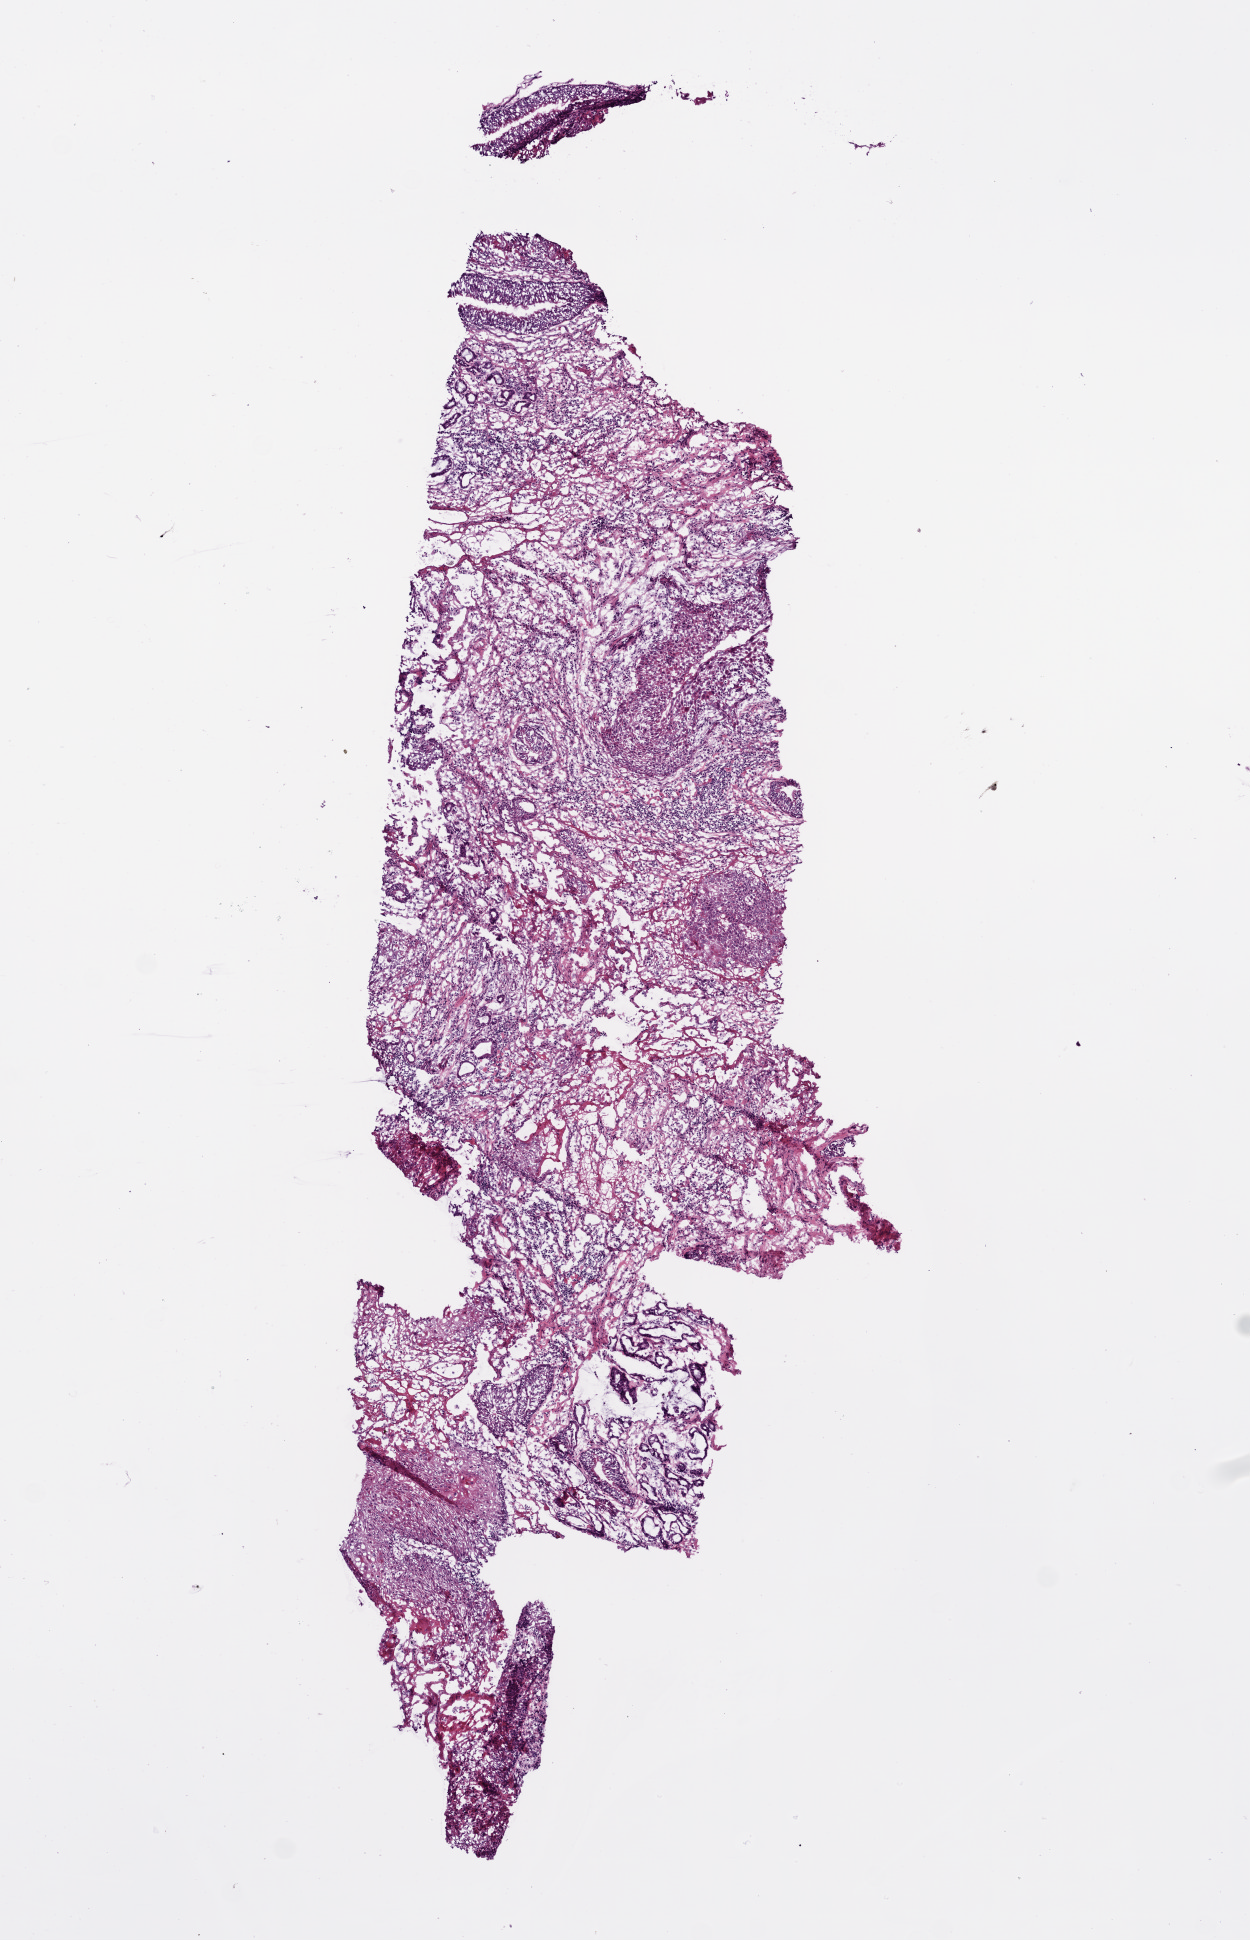
Whole-slide histology image, Hematoxylin and eosin (H&E) stained — a low-resolution overview of the entire scanned area, about 5.0 x 7.8 mm (acquisition: 20x scan); frozen section from the bottom of the tissue portion; sample: primary tumour, head and neck. Male, age 53 years at initial diagnosis. Histologic grade: G2 (moderately differentiated). Pathologist review of this section (percent, as recorded): tumour cells 50%, tumour nuclei 40%, normal cells 5%, stromal cells 40%, necrosis 0%. Inflammatory infiltration, as recorded: lymphocyte infiltration 40%, monocyte infiltration 0%, neutrophil infiltration 0%.
- lymph nodes positive (case pathology): 0 of 39 examined
- AJCC pathologic stage: IVA (6th edition)
- diagnosis: Squamous cell carcinoma, NOS (larynx, NOS)